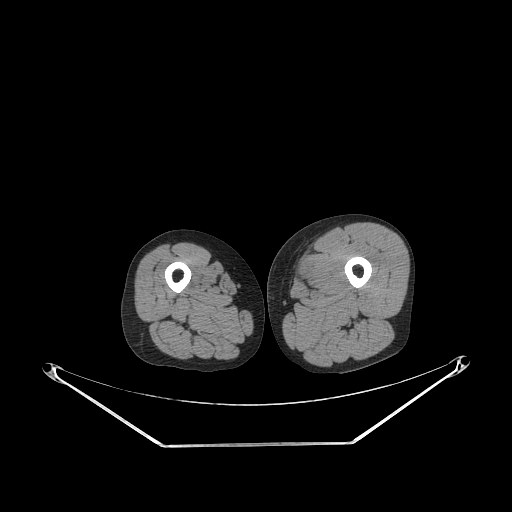
CT of an extremity soft-tissue mass (from a PET/CT study), one axial slice; slice 233 of 267 in the series (ordered by position); reconstruction kernel STANDARD; soft-tissue window (W 400 / L 40 HU); 3.75 mm slice thickness; 512 × 512 image matrix. Male patient. Case-level facts recorded for this patient, not image findings: histological type: pleiomorphic leiomyosarcoma; grade: high; site of the primary tumour: left thigh.
Outlined on this slice (expert contour drawn on MRI and transferred to this co-registered scan by the dataset authors):
- gross tumour volume including surrounding oedema: box from (x=290, y=260) to (x=312, y=289) px